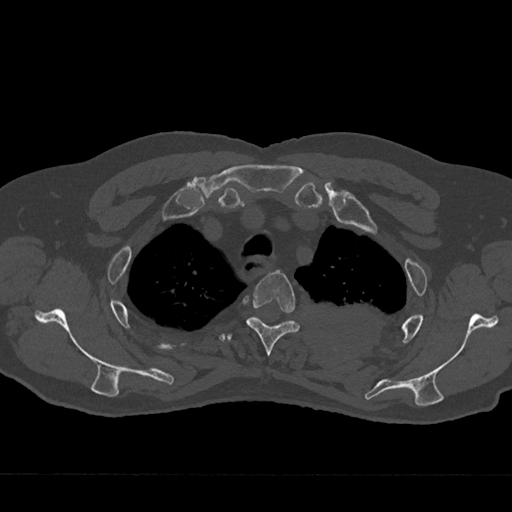
CT including the spine, one axial slice; slice 564 of 797 in the series (ordered by position); reconstruction kernel Br40s/3; bone window (W 1800 / L 400 HU); 512 × 512 image matrix, field of view 377 × 377 mm. Patient: male, 75 years. Case-level facts recorded for this patient, not image findings: primary cancer: renal; vertebrae with lytic lesions (as recorded): T4.
Outlined on this slice (semi-automatically segmented with operator editing):
- T3 vertebra: box from (x=246, y=270) to (x=300, y=356) px
- T4 vertebra: (x=227, y=322)–(x=285, y=341)